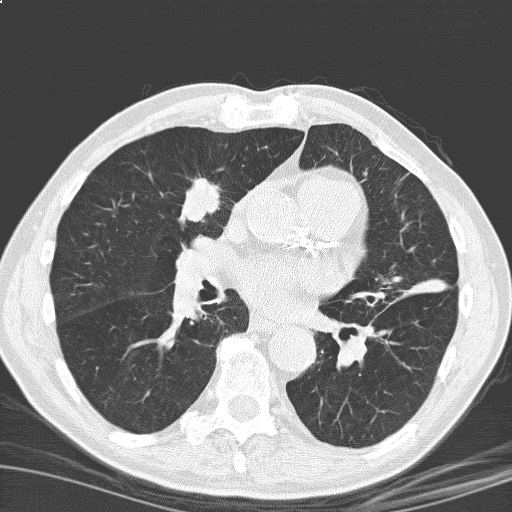
Low-dose screening chest CT, one axial slice. Position 94 of 184 along the scan axis. Lung window (W 1500 / L -600 HU). 3.2 mm slice thickness. 512 × 512 image matrix, field of view 329 × 329 mm.
Outlined on this slice (expert manual segmentation):
- lesion 1 (tumor, upper lobe of right lung): box from (x=181, y=178) to (x=219, y=222) px